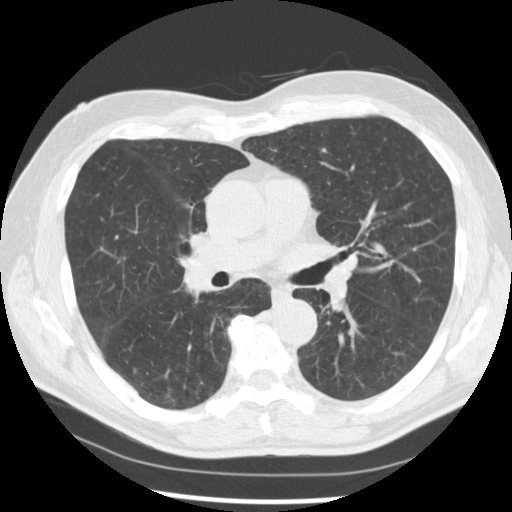
Low-dose screening chest CT, one axial slice. Position 160 of 277 along the scan axis. Lung window (W 1500 / L -600 HU). 2.5 mm slice thickness. 512 × 512 image matrix, field of view 365 × 365 mm.
Structures marked on this image (manually delineated by an expert):
- lesion 1 (tumor, middle lobe of right lung): bounding box (x1, y1, x2, y2) in pixels: (183, 262, 212, 300)